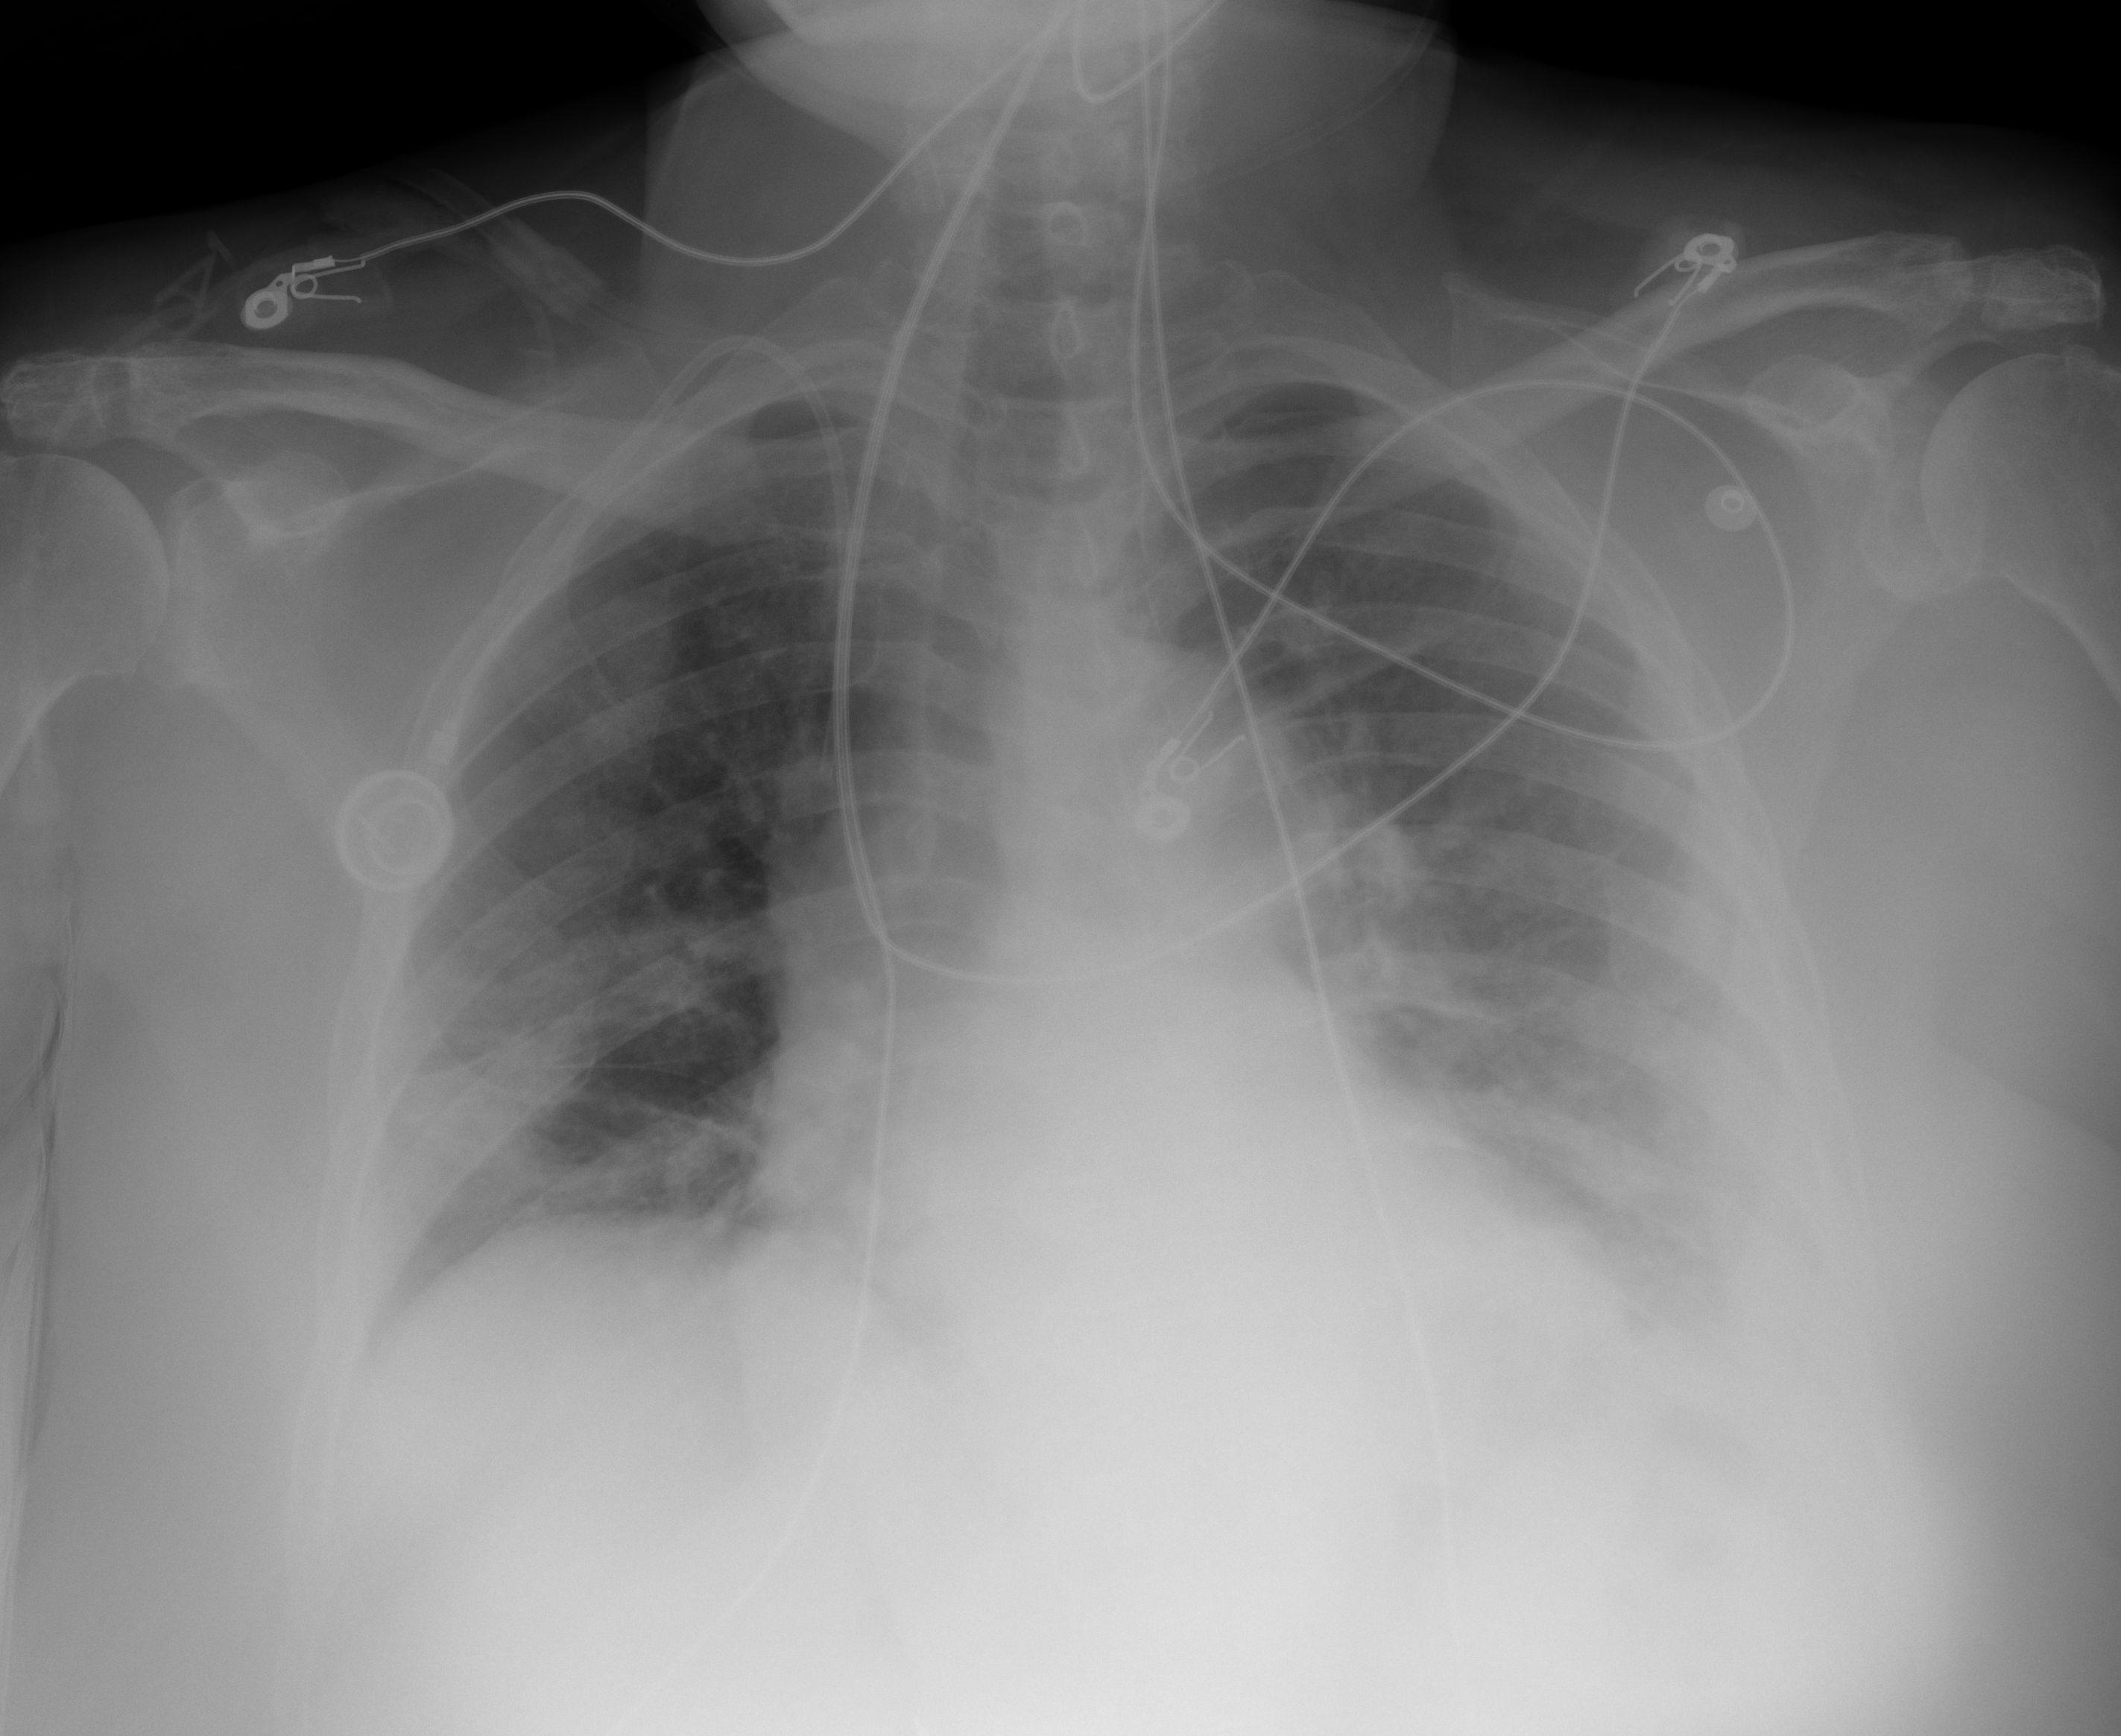
Portable chest radiograph, AP projection. Female patient, age 76 years; imaged 3 days after the COVID-19 diagnosis.
Radiologist key findings (as recorded): Diffuse bibasilar haziness with possible trace pleural effusion.